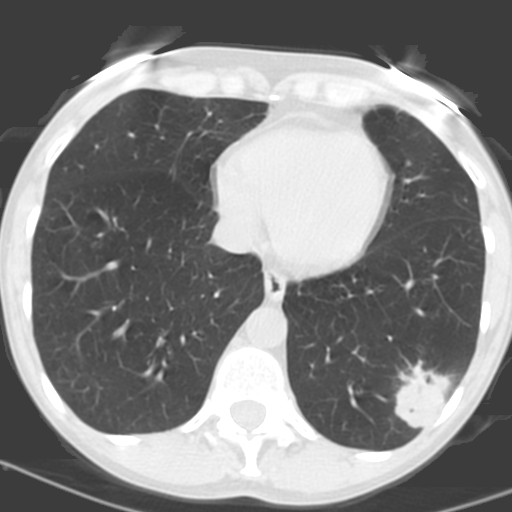
Low-dose screening chest CT, one axial slice. Slice 51 of 156 in the series (ordered by position). 120 kVp. Lung window (W 1500 / L -600 HU). 3.2 mm slice thickness. 512 × 512 image matrix.
Annotated regions visible in this slice (manually delineated by an expert):
- lesion 1 (tumor, lower lobe of left lung): bounding box (x1, y1, x2, y2) in pixels: (395, 360, 452, 429)